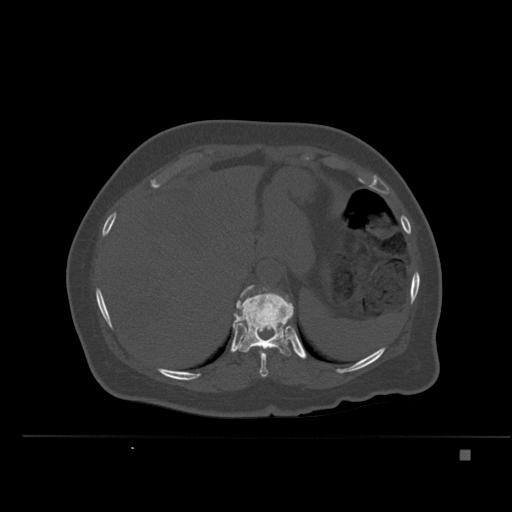
CT including the spine, one axial slice. Position 271 of 477 along the scan axis. Bone window (W 1800 / L 400 HU). 512 × 512 image matrix, field of view 422 × 422 mm. Patient: female, 74 years. From the clinical record (not read from this slice): primary cancer: colon.
Outlined on this slice (semi-automatic segmentation, software-assisted and operator-edited):
- T10 vertebra: bounding box [x1, y1, x2, y2] px = [254, 346, 268, 377]
- T11 vertebra: [233, 285, 294, 356]
- T12 vertebra: [264, 288, 267, 290]